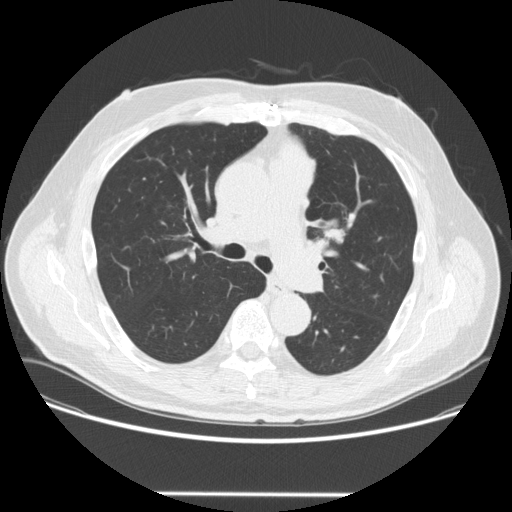
Axial slice from a low-dose chest CT screening exam; third screening round (two years after baseline); lung window (W 1500 / L -600 HU); 2.5 mm slice thickness; slice 89 of 253 in the series; 512 × 512 image matrix. Male participant, aged 66 years at enrolment. Former smoker at enrolment.
• Expert reader's lesion annotation, bounding box (x1, y1, x2, y2) in pixels: (310, 204, 362, 253).
• The screening reader recorded 2 non-calcified nodules or masses ≥4 mm on this exam (left upper lobe, right lower lobe); which of them this box marks is not recorded.
• Official screen result: positive, other.
• Lung cancer was diagnosed 85 days after this screen: squamous cell carcinoma, NOS, left upper lobe, poorly differentiated (G3), stage IA (AJCC 6th edition), 27 mm at pathology.